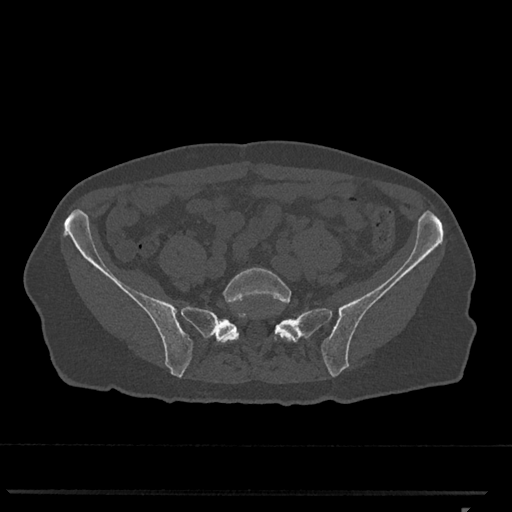
CT including the spine, one axial slice; position 123 of 793 along the scan axis; reconstruction kernel Br40s/3; 120 kVp; bone window (W 1800 / L 400 HU); 0.5 mm slice thickness; 512 × 512 image matrix. Patient: female, 62 years. Case-level facts recorded for this patient, not image findings: primary cancer: renal.
Outlined on this slice (semi-automatic segmentation, software-assisted and operator-edited):
- L5 vertebra: bounding box [x1, y1, x2, y2] px = [219, 268, 297, 343]